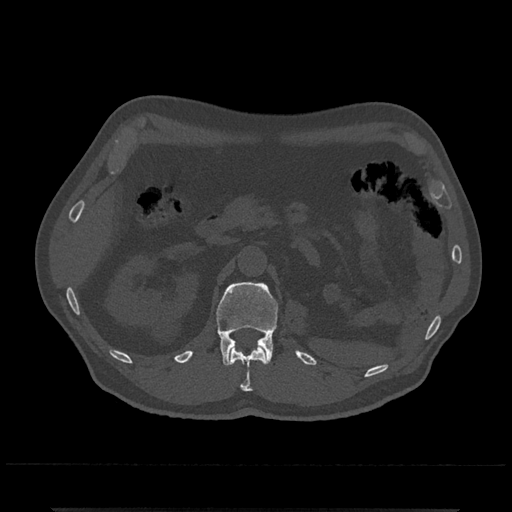
CT including the spine, one axial slice; reconstruction kernel Br40s/3; bone window (W 1800 / L 400 HU); 0.5 mm slice thickness; 512 × 512 image matrix, field of view 393 × 393 mm. Male patient, age 67 years. Case-level facts recorded for this patient, not image findings: primary cancer: prostate.
Outlined on this slice (semi-automatically segmented with operator editing):
- L1 vertebra: bounding box <216,282,278,366> (left, top, right, bottom; pixels)
- T12 vertebra: <230,346,267,391>